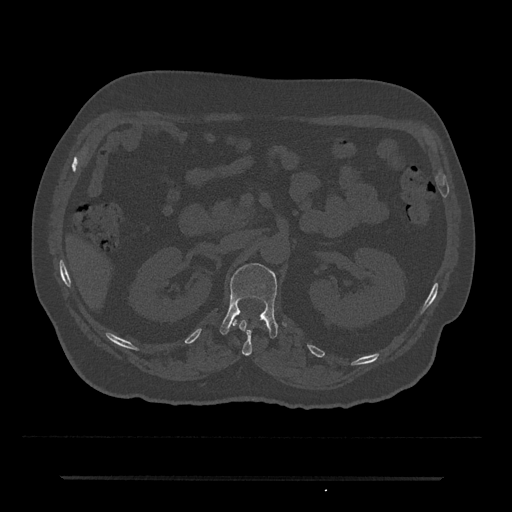
CT including the spine, one axial slice; slice 89 of 797 in the series (ordered by position); 120 kVp; bone window (W 1800 / L 400 HU); 0.5 mm slice thickness; 512 × 512 image matrix, field of view 437 × 437 mm. Patient: male, 69 years. Case-level facts recorded for this patient, not image findings: primary cancer: prostate.
Structures marked on this image (semi-automatically segmented with operator editing):
- L1 vertebra: bounding box <219,263,278,339> (left, top, right, bottom; pixels)
- T12 vertebra: <232,315,267,356>